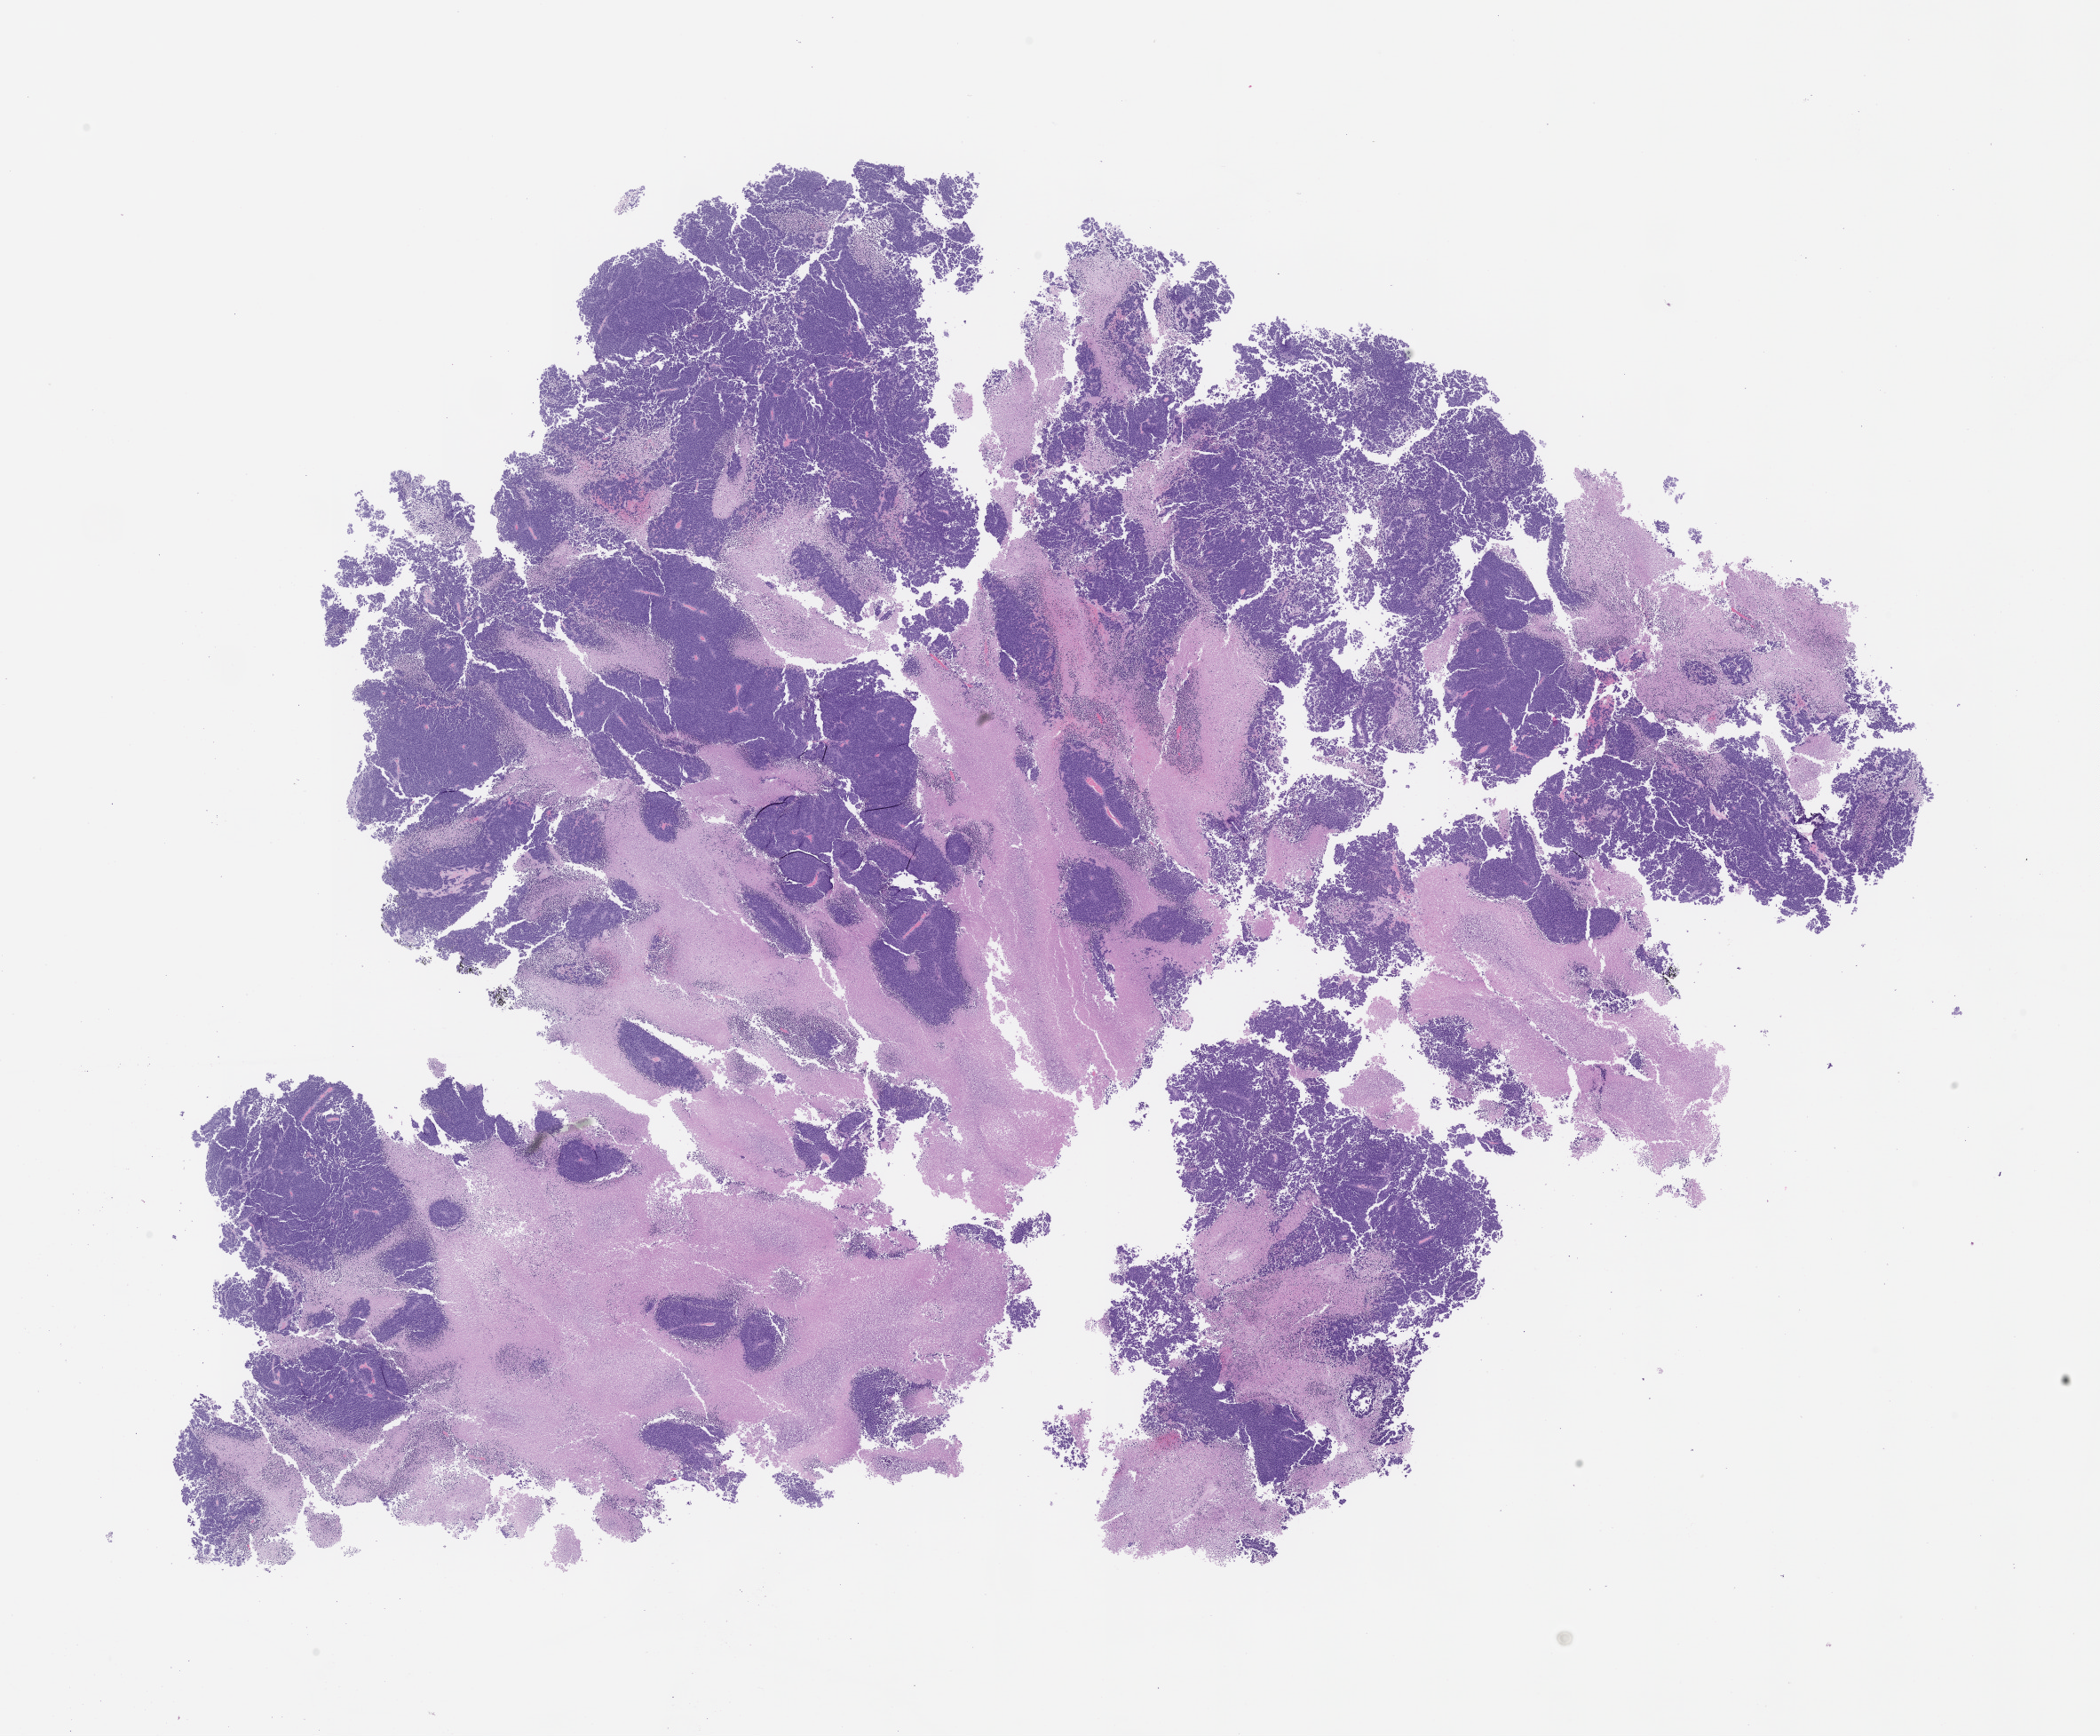
Whole-slide image, haematoxylin and eosin: patient-derived xenograft (human tumor grown in a mouse), passage 1 — low-resolution overview of the scanned area, about 18.9 x 15.7 mm, formalin-fixed paraffin-embedded section, originating tumor site category: bladder.
Originating patient diagnosis: Urothelial Carcinoma.